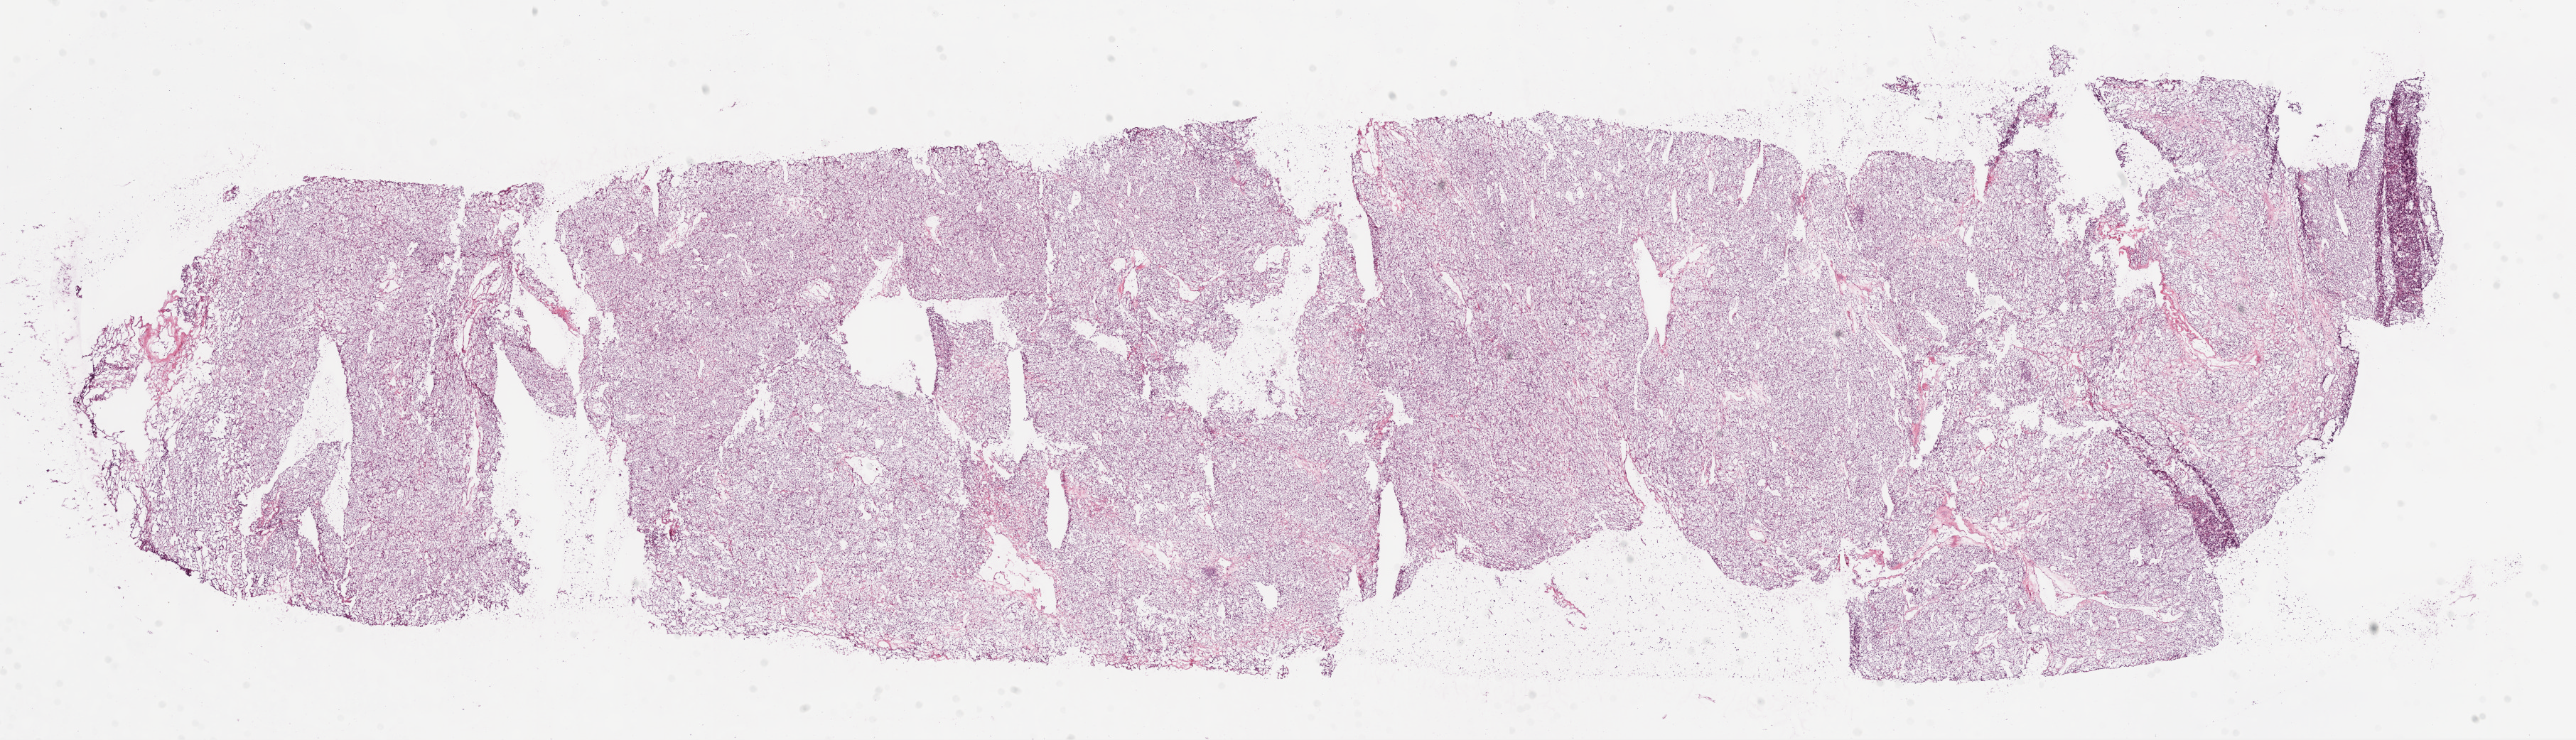
Digitized Hematoxylin and eosin (H&E) stained tissue section (whole slide), shown as a low-resolution overview of the whole scanned area (about 29.1 x 8.4 mm, from a 20x scan). Frozen section. Kidney, primary tumour sample. Female, age 58 years at initial diagnosis. Composition of this section per pathologist review: tumour cells 95%, tumour nuclei 90%.
Pathologic diagnosis: Clear cell adenocarcinoma, NOS.